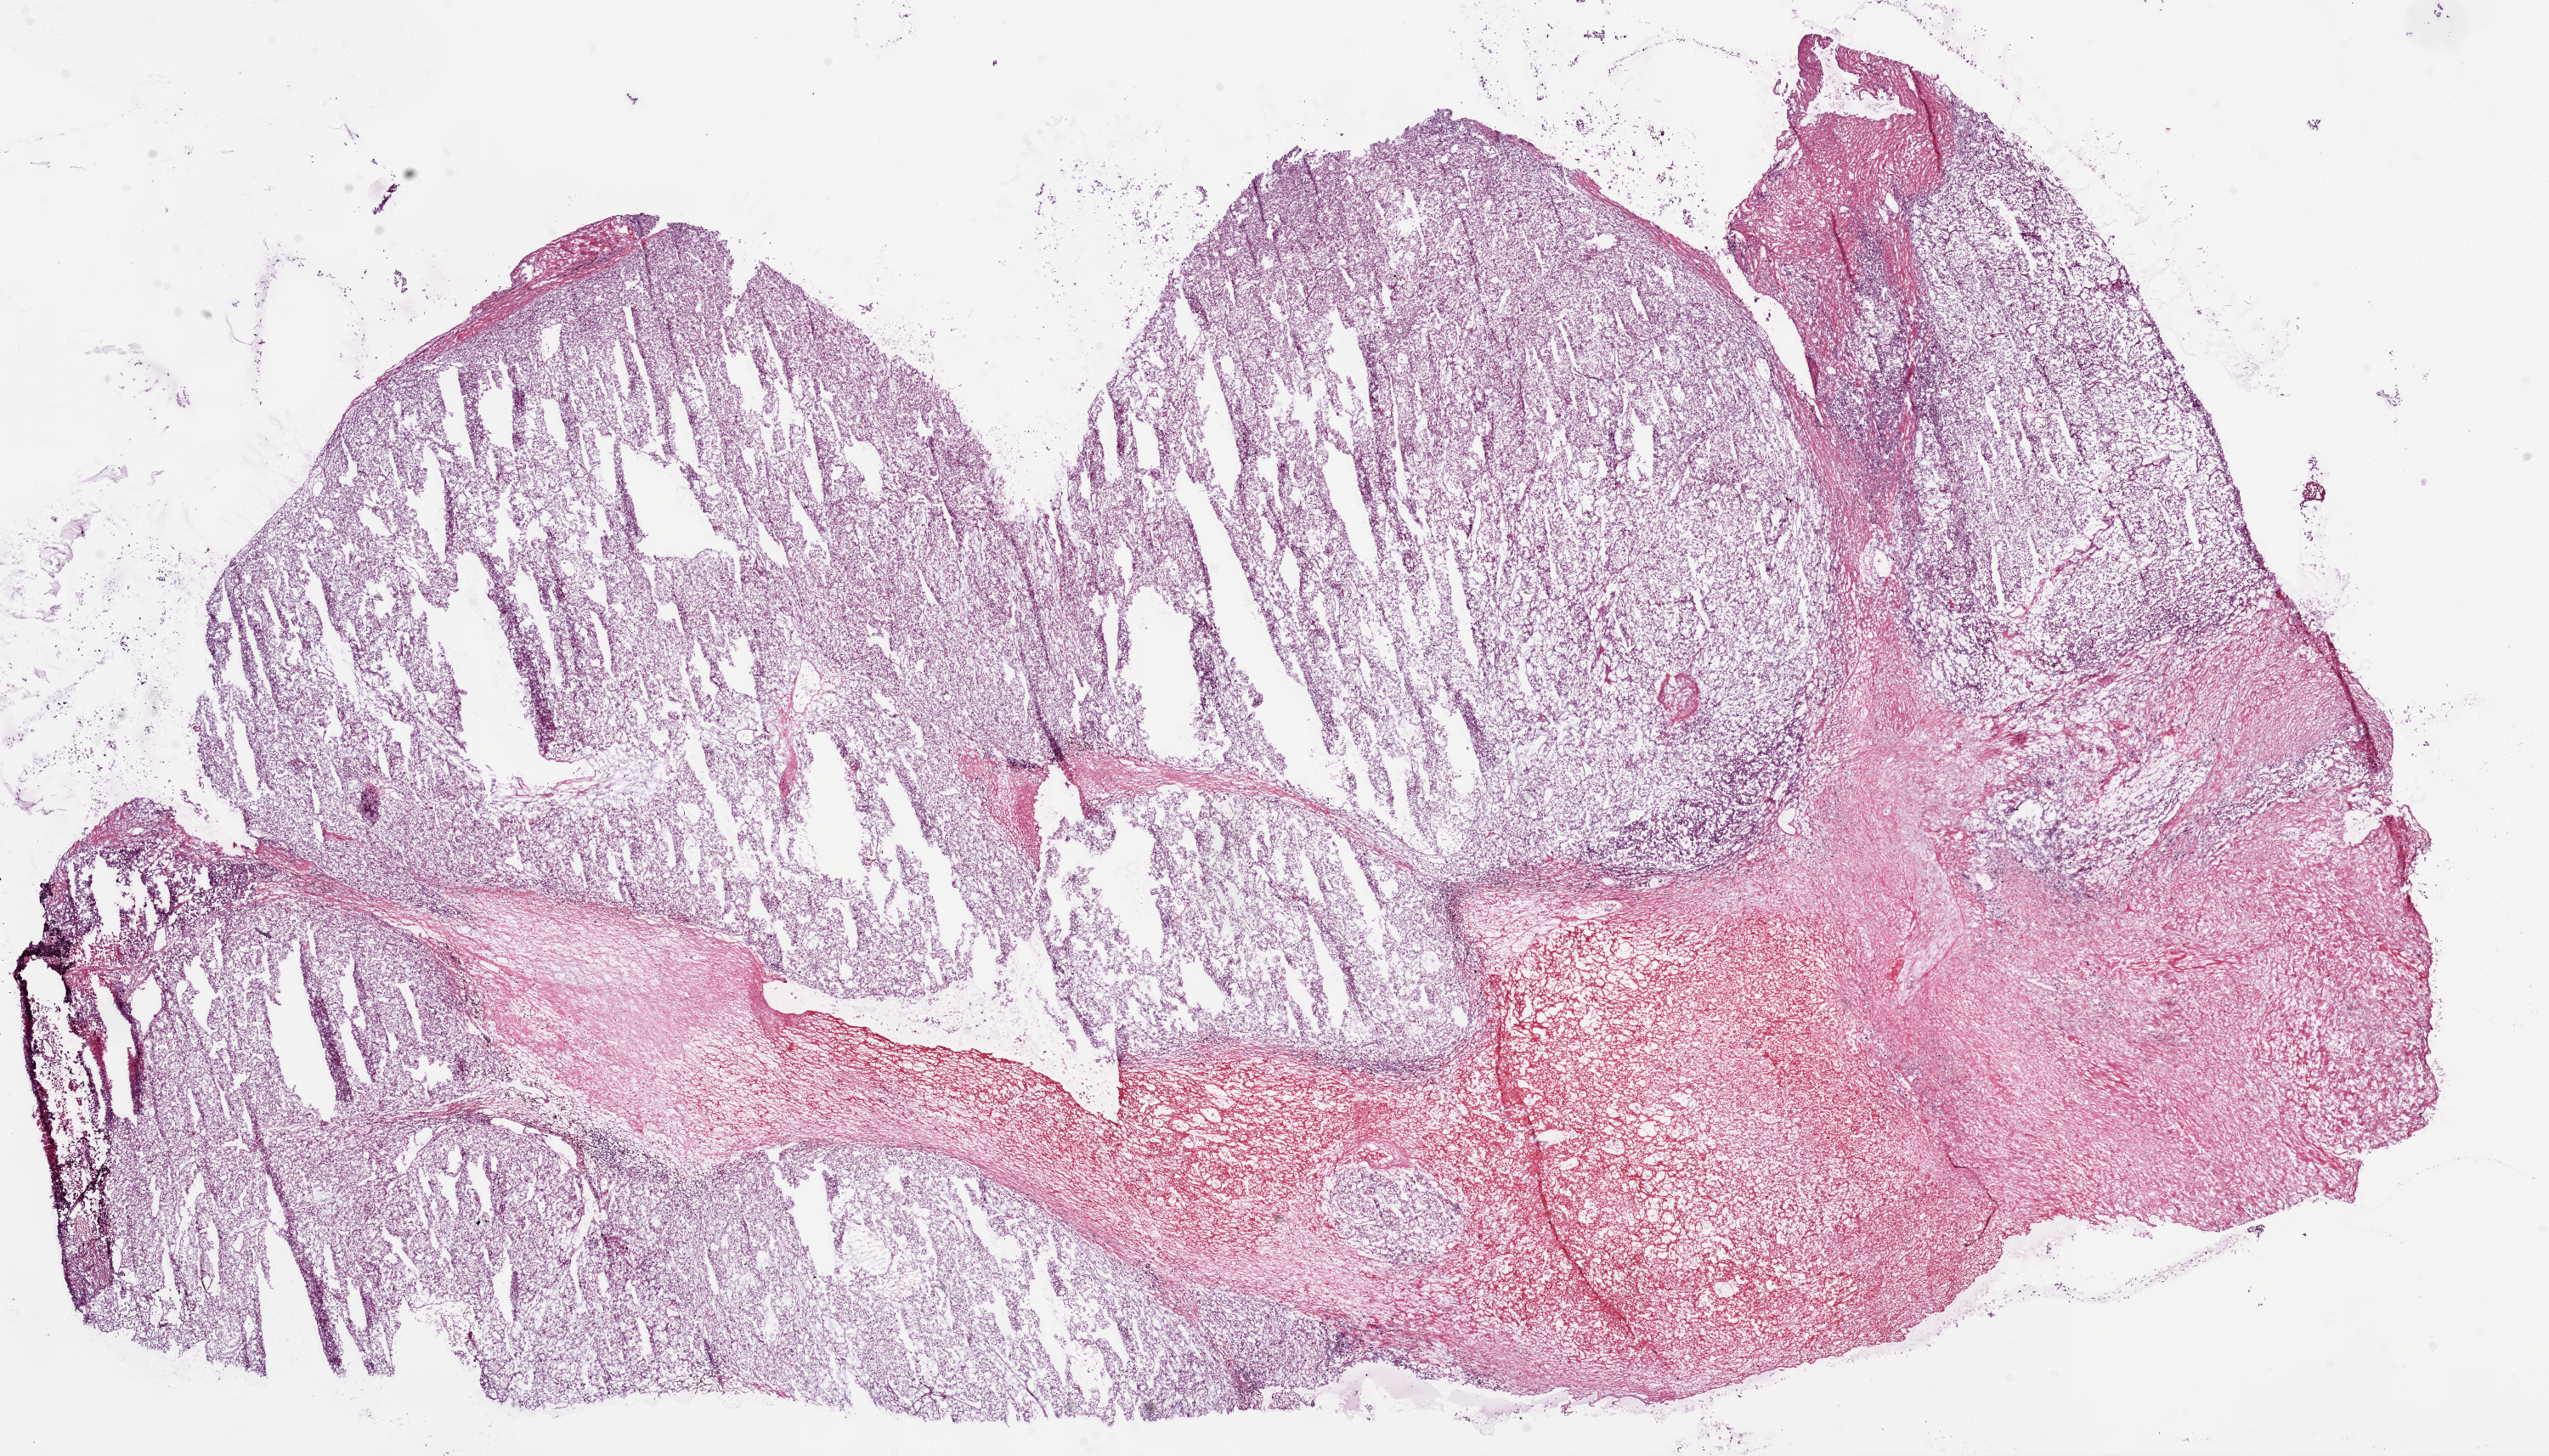
Digitized Hematoxylin and eosin (H&E) stained tissue section (whole slide) — a low-resolution overview of the entire scanned area, about 24.1 x 13.8 mm; frozen section; sample: primary tumour, kidney. Patient: female, age at initial diagnosis 77 years. Pathologist review of this section (percent, as recorded): tumour cells 70%, tumour nuclei 85%.
Diagnosis: Clear cell adenocarcinoma, NOS.